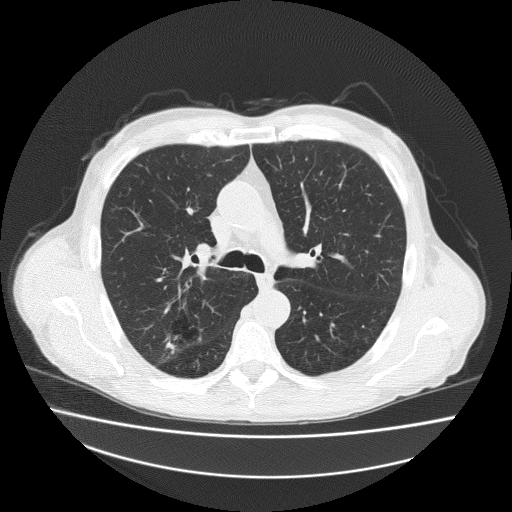
Low-dose screening chest CT, axial slice; second annual screen; lung window (W 1500 / L -600 HU); 2 mm slice thickness; slice 73 of 186 in the series; 512 × 512 image matrix. Male participant, aged 73 years at enrolment. Current smoker at enrolment.
Expert-annotated lung lesion, bounding box [x1, y1, x2, y2] px = [155, 311, 209, 352]. Screening reader's record for this exam: no non-calcified nodule ≥4 mm recorded. Later outcome: lung cancer diagnosed 418 days after this screen (after the third annual screen) — adenosquamous carcinoma, right upper lobe, well differentiated (G1), stage IA (AJCC 6th edition), 20 mm at pathology.